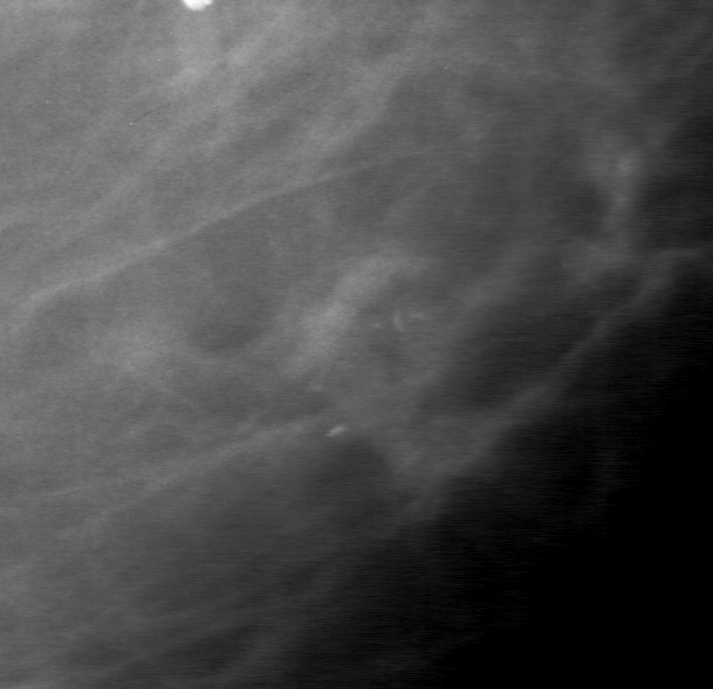
Region of interest cut from a scanned film mammogram (one marked finding), left breast, CC view, BI-RADS breast density category 1 (scale 1–4).
Finding: calcifications, morphology fine linear branching, distribution clustered; BI-RADS assessment category 3; pathology result (as recorded, not read from the image): malignant.